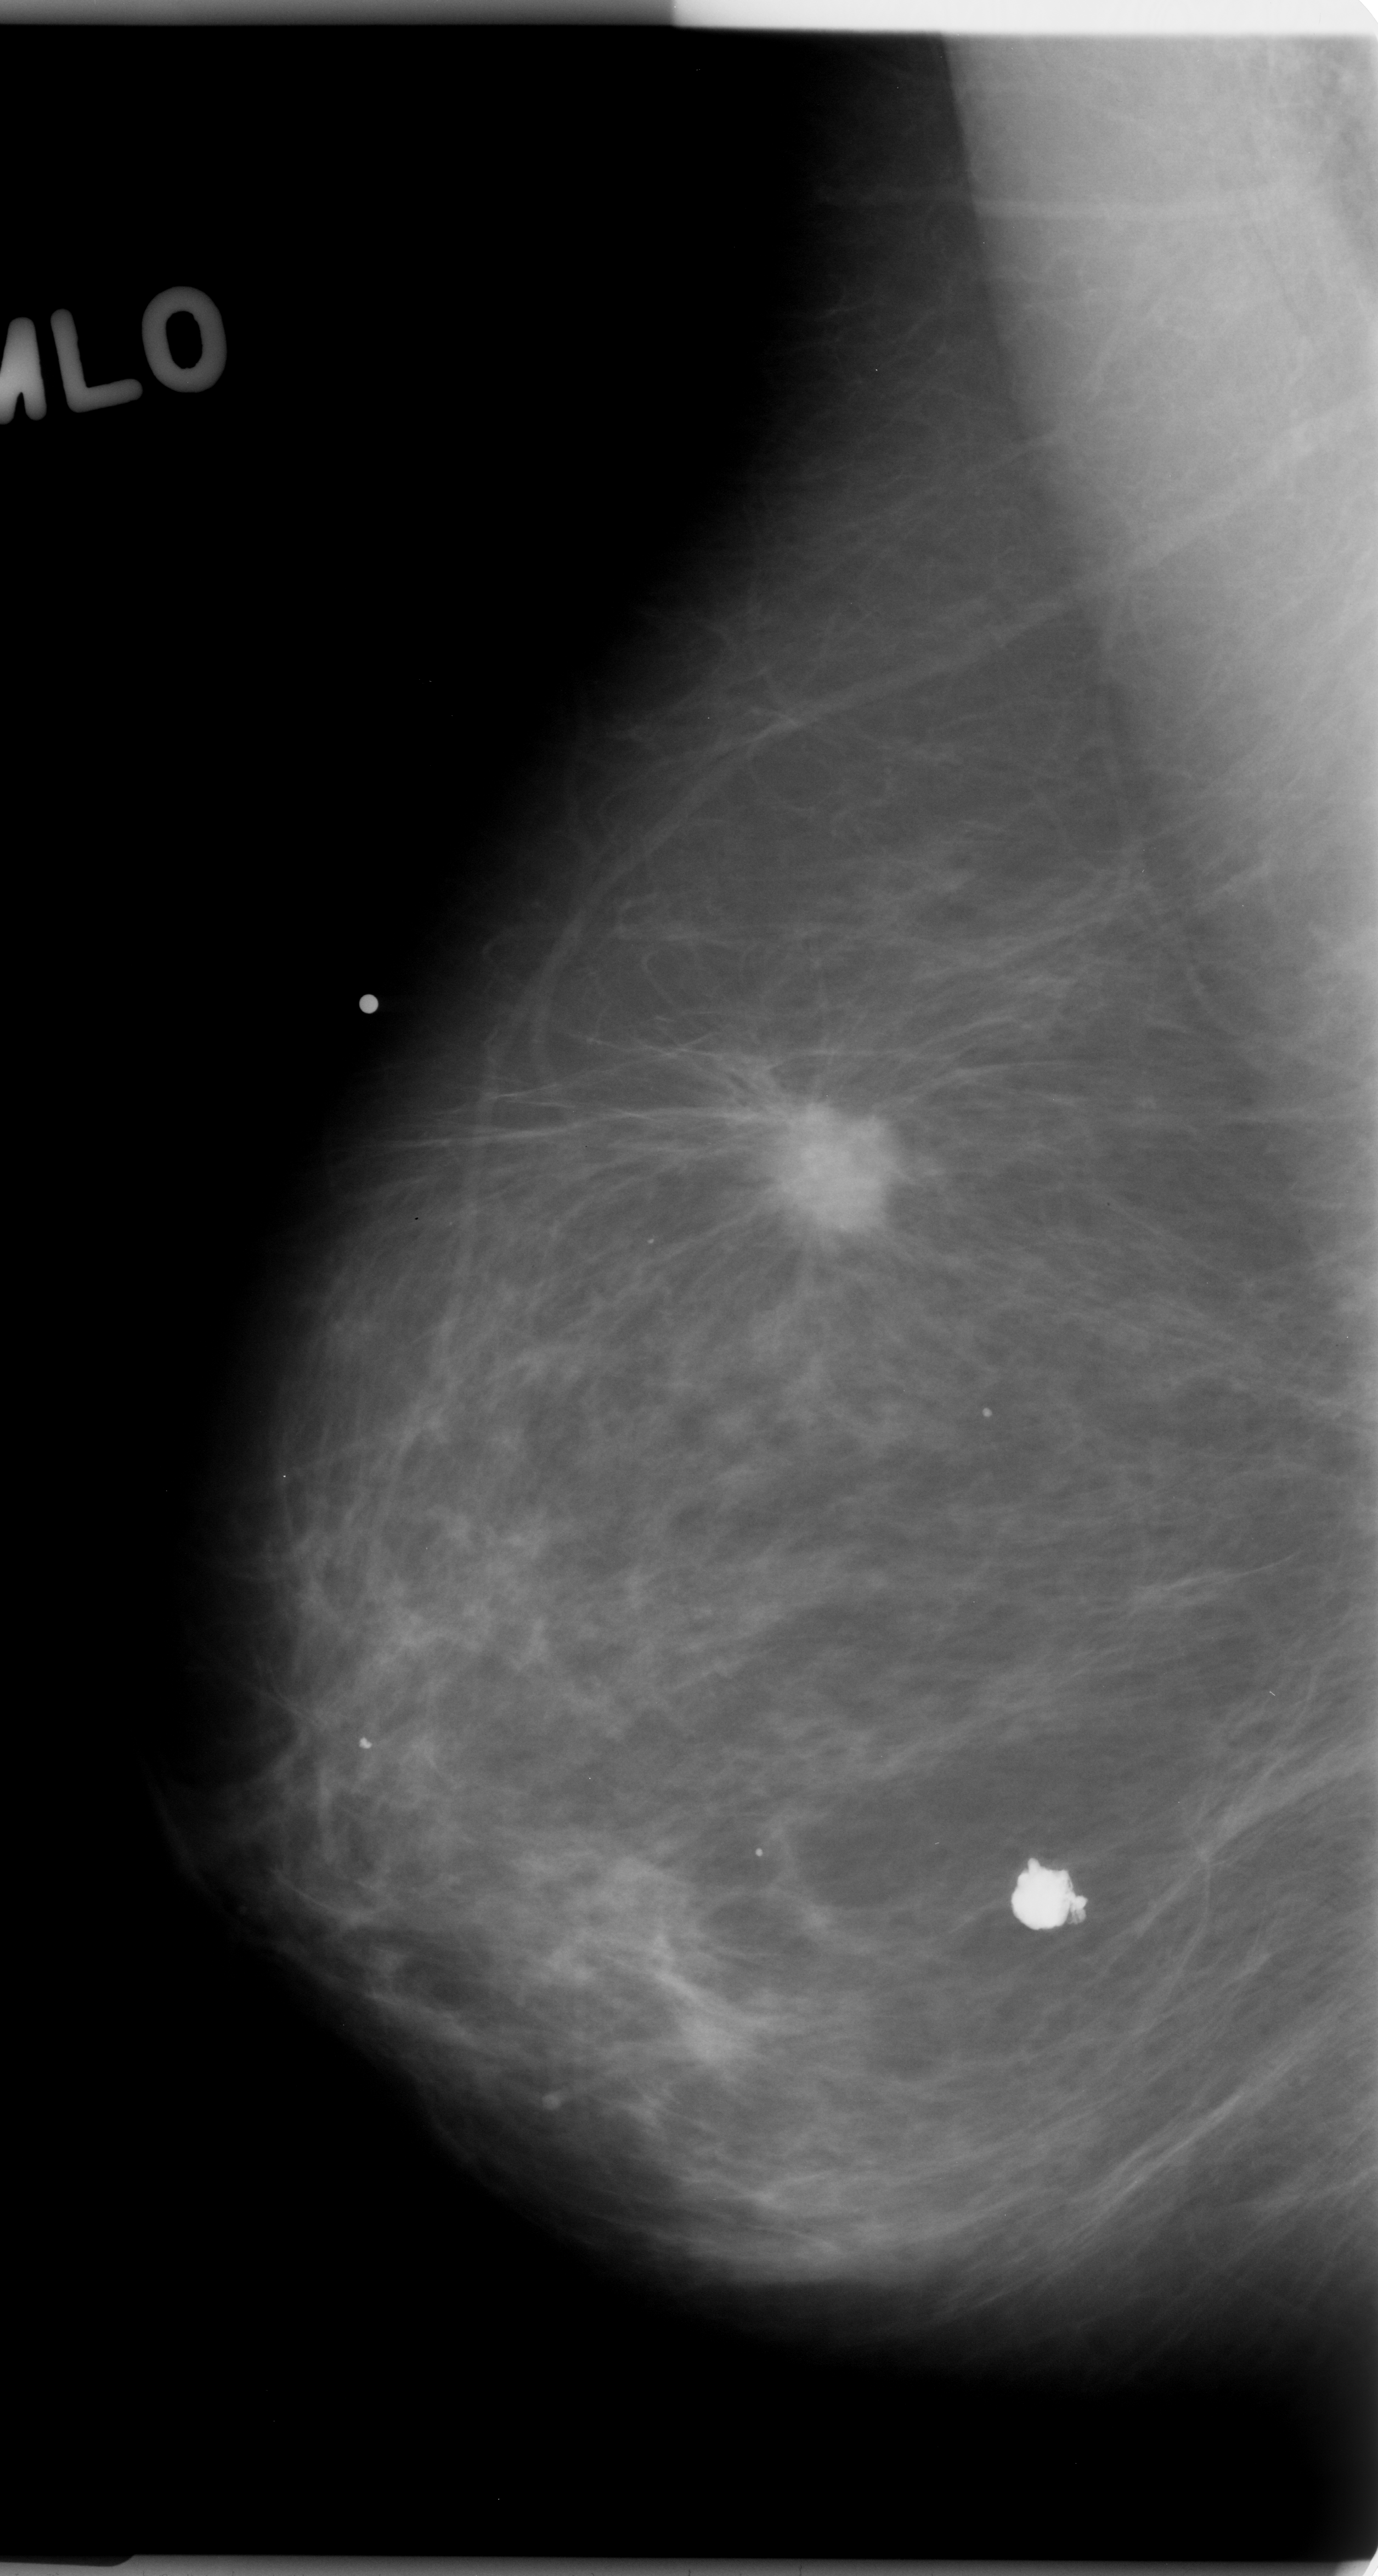
Digitized screen-film mammogram, right breast, mediolateral oblique (MLO) view, breast composition: almost entirely fatty (BI-RADS density category 1 of 4).
Abnormality record for this image: mass, shape irregular, margins spiculated; BI-RADS assessment category 5; pathology (as recorded): malignant.